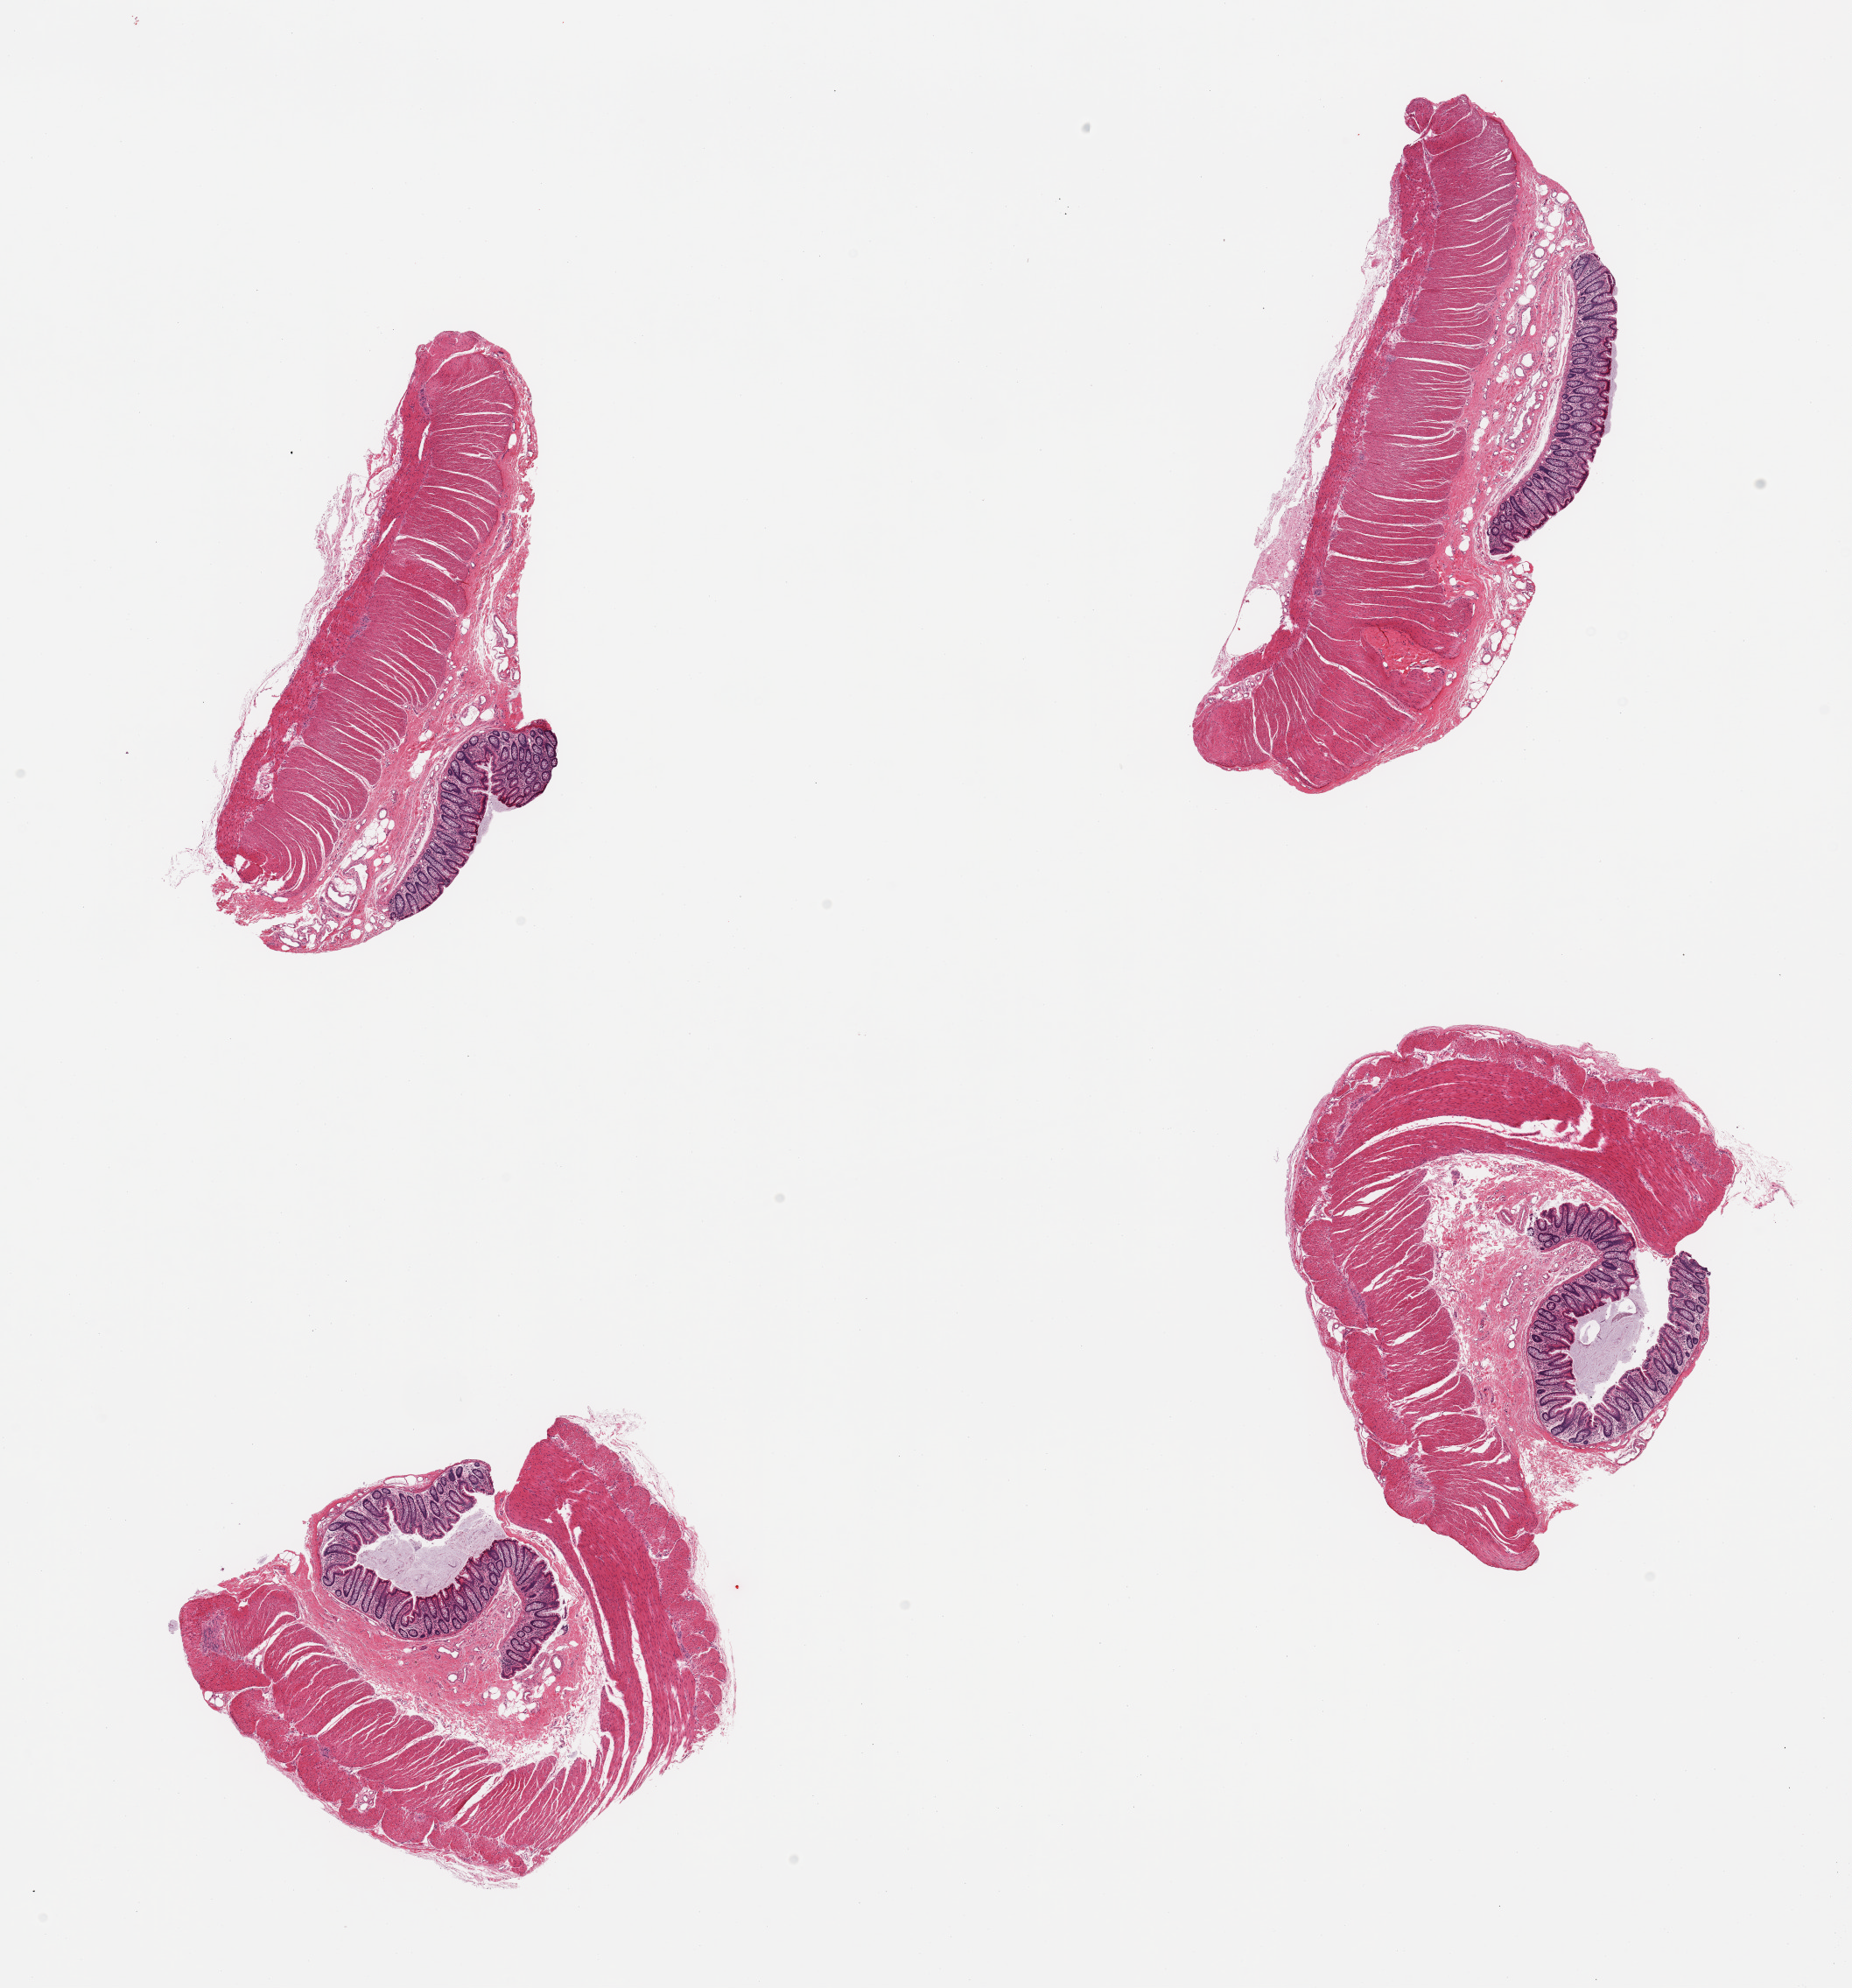
Digitized haematoxylin and eosin-stained section, whole scanned area (about 16.7 x 18.0 mm, slide scanned at 20x) shown as a low-resolution overview; PAXgene-fixed, paraffin-embedded tissue; target tissue: transverse colon; tissue donor sample. Donor sex: female.
Review note (as recorded): 4 pieces, mucosa up to ~0.4mm, ~15% thickness, well preserved.